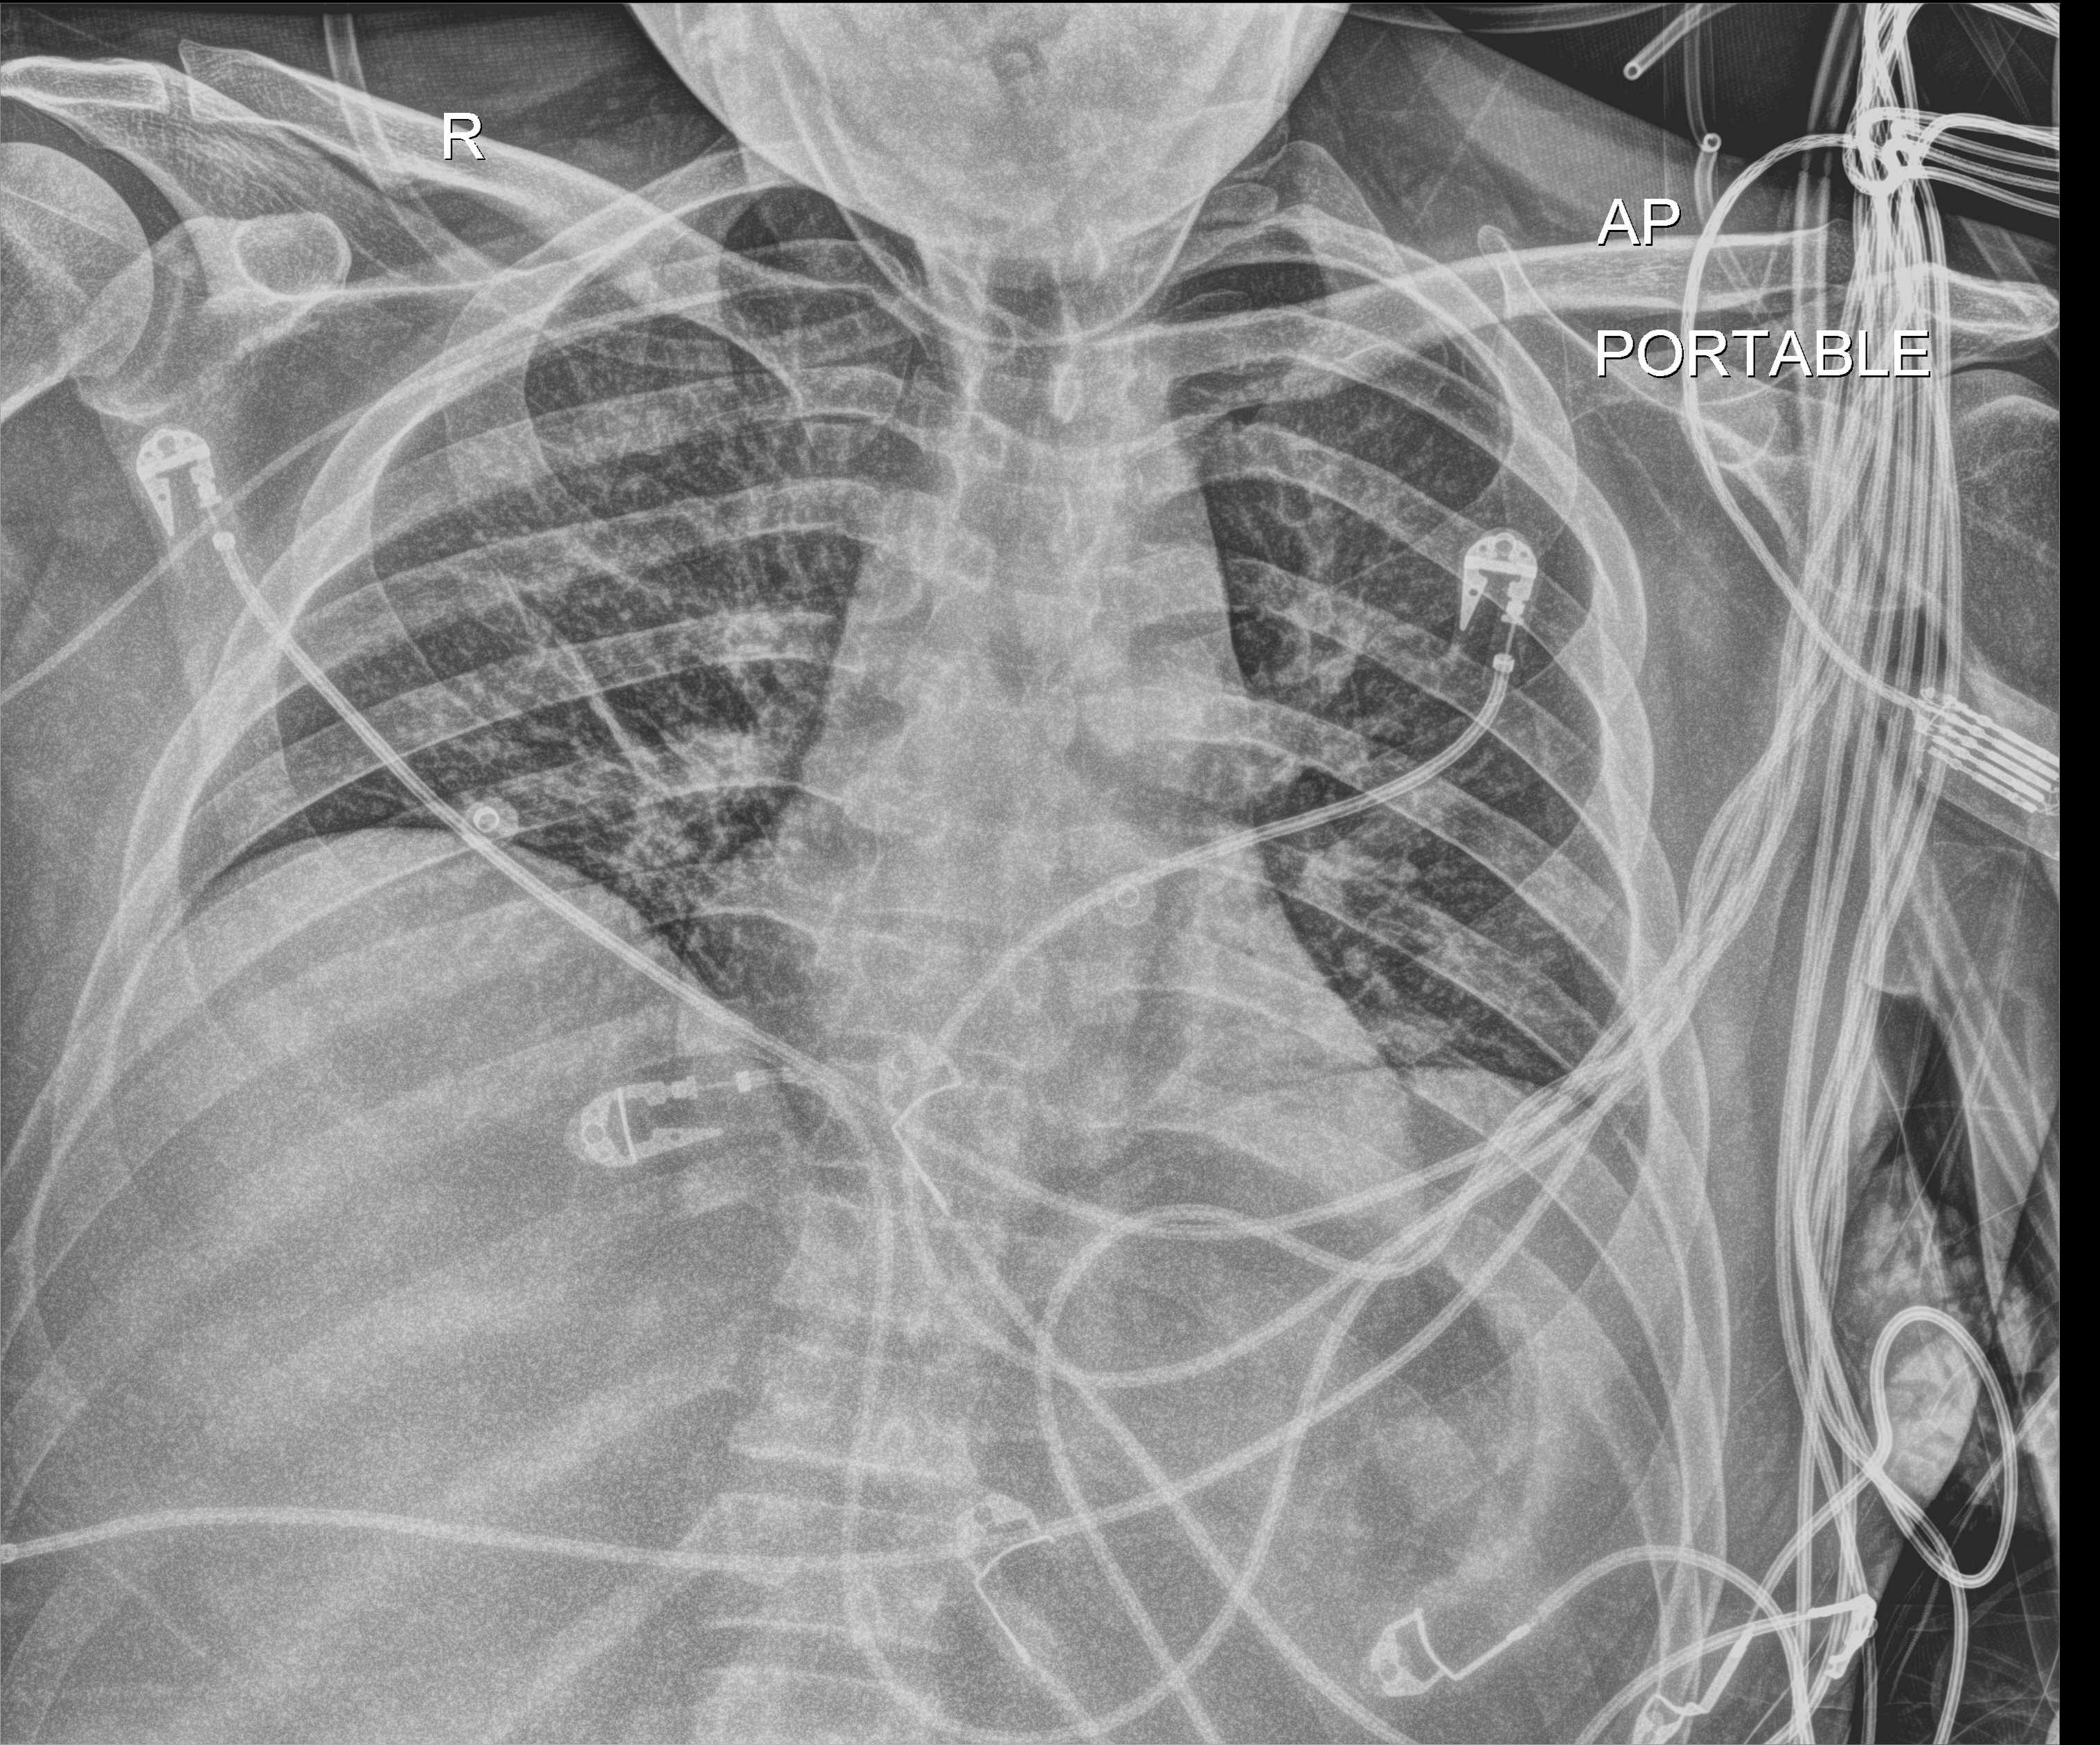
Bedside chest radiograph (digital radiography). Patient hospitalised with COVID-19; male, aged 18–59 years.
From the hospital-stay record, not from the radiograph (when in the stay this image was taken is not recorded):
- hypertension (admission record): yes
- length of hospital stay: 61 days
- mechanically ventilated during this hospital stay: yes